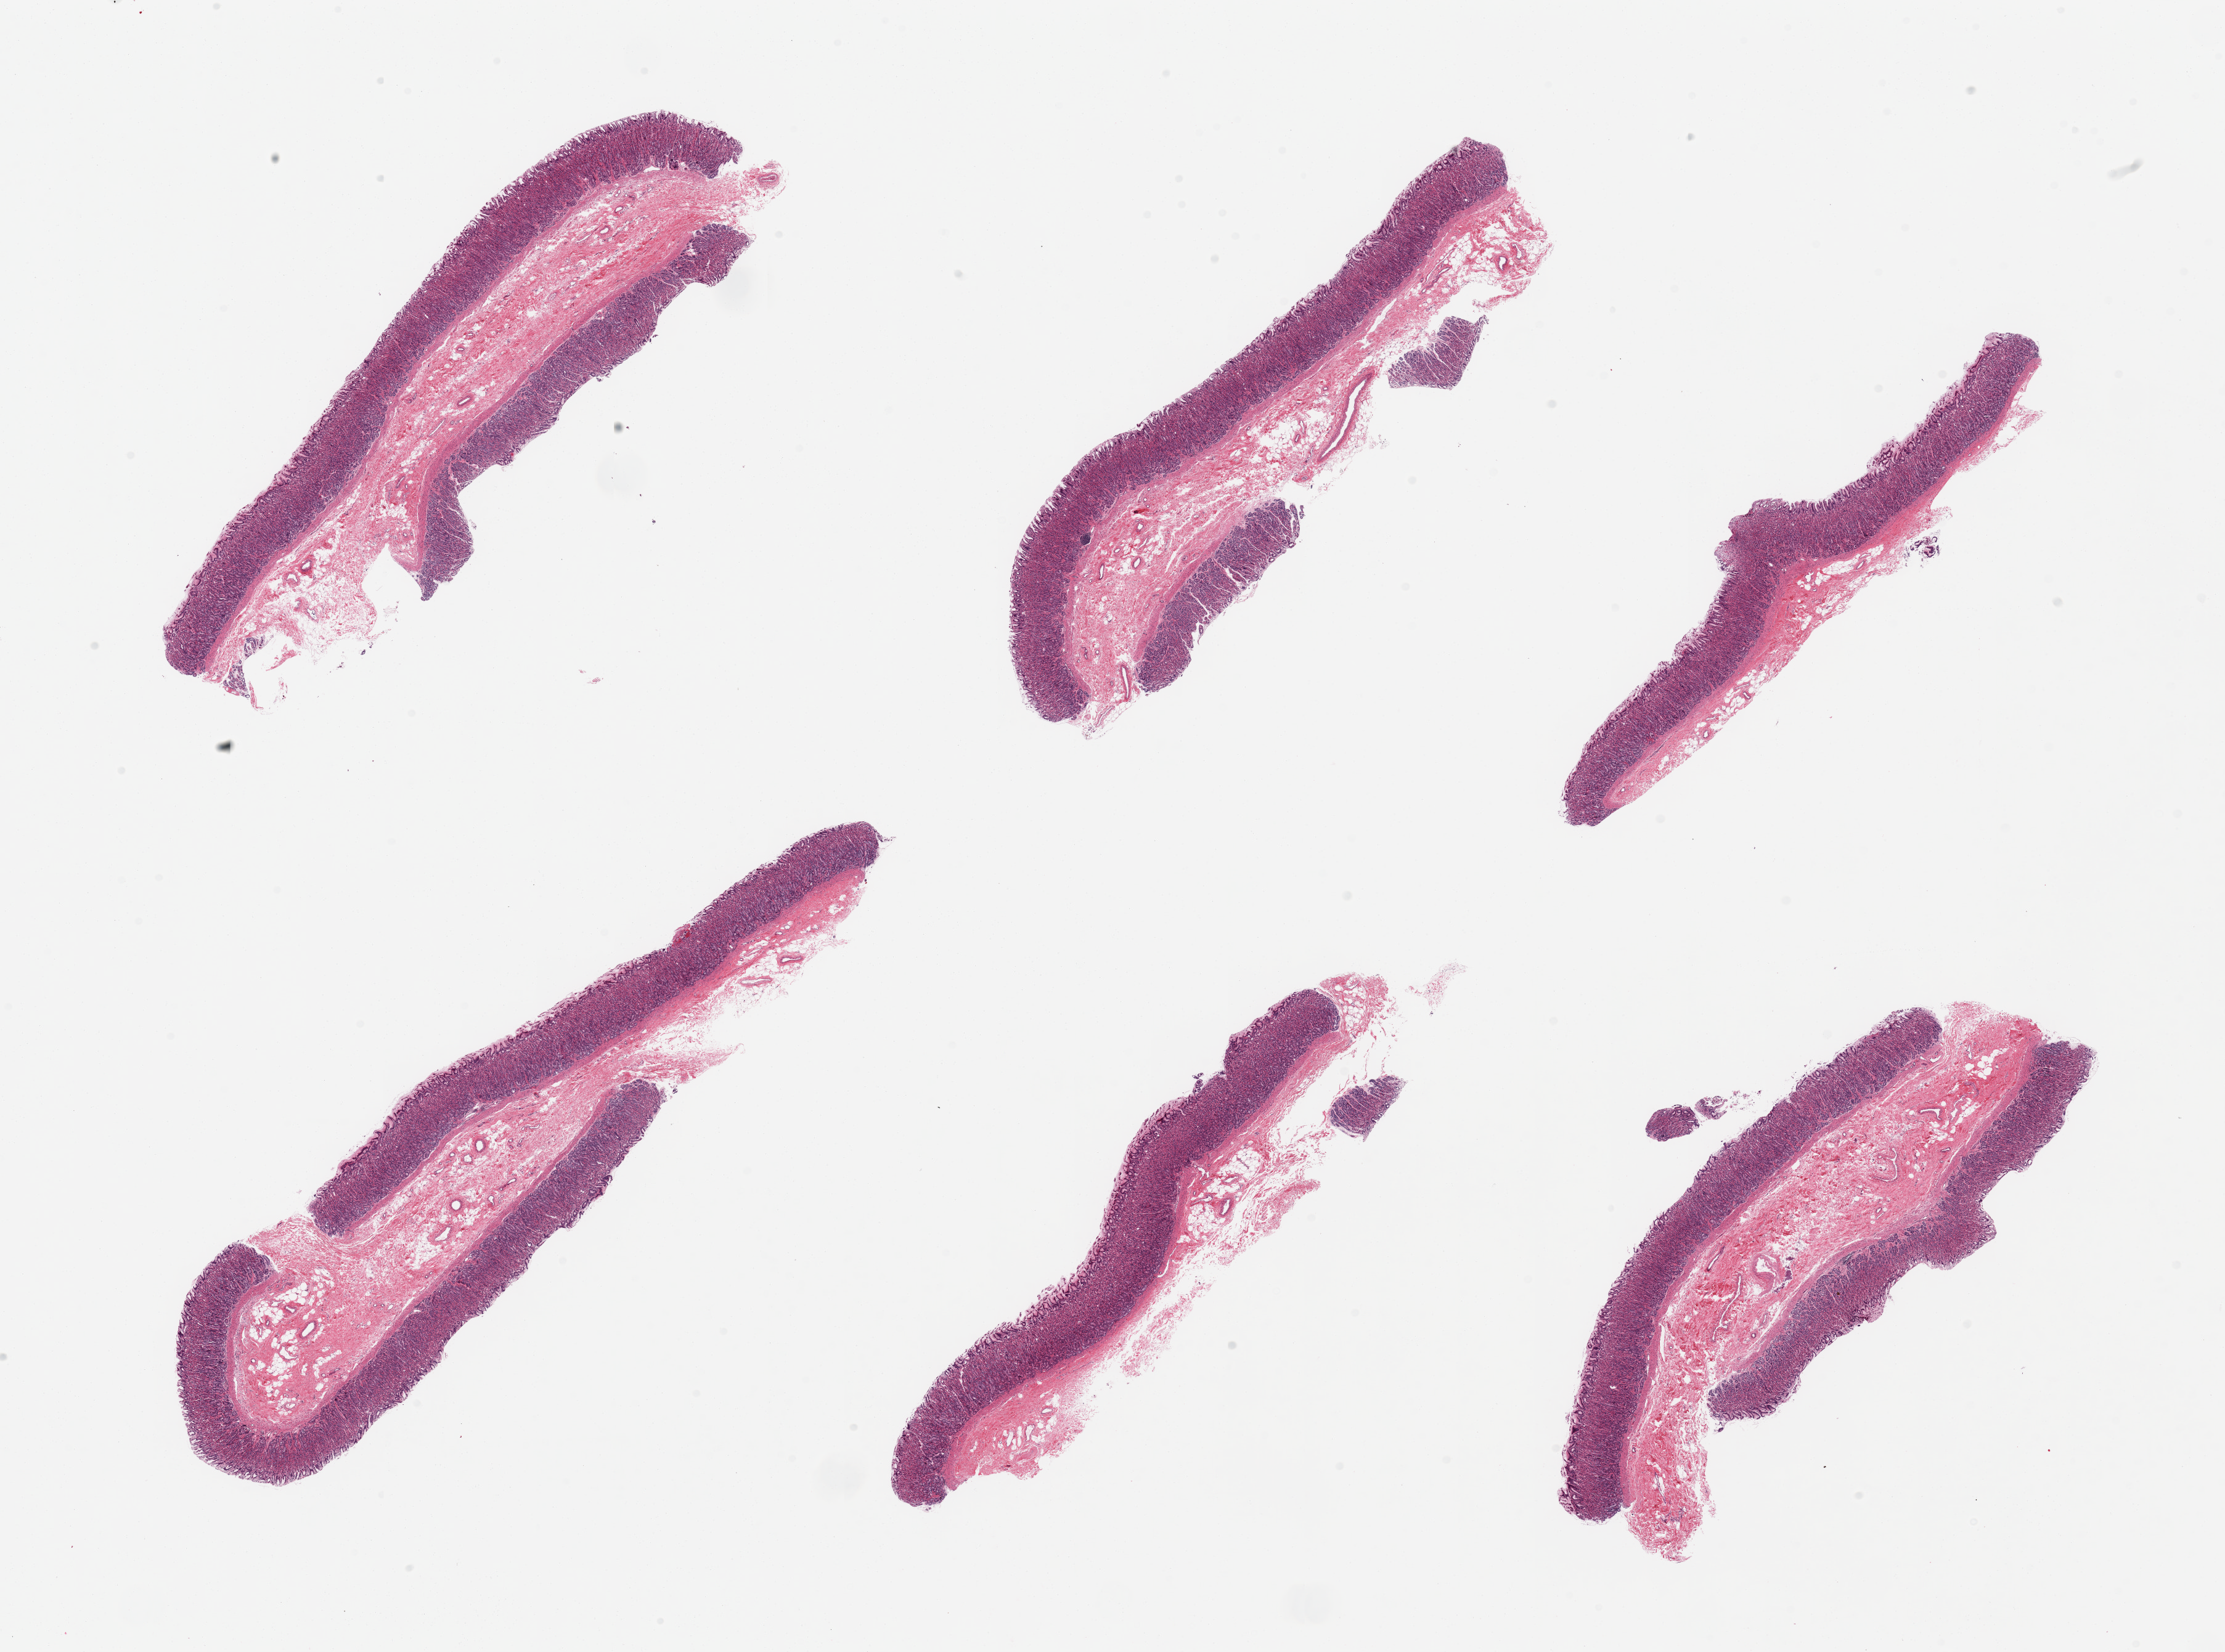
H&E whole-slide image — whole scanned area (about 28.5 x 21.2 mm, slide scanned at 20x) shown as a low-resolution overview; PAXgene-fixed, paraffin-embedded tissue; target tissue: stomach; donor tissue sample. Female donor.
Review note (as recorded): 6 pieces, mucosa well-preserved, good specimens, up to ~0.8mm, ~35-50% of thickness.